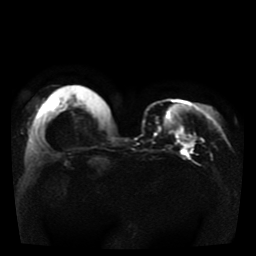
Breast MRI, one axial slice. Slice 12 of 41 in the series (ordered by position). Diffusion-weighted series; image 2 of 4 stored at this slice position (different b-values; order by instance number). 1.5 T. 5 mm slice thickness. 256 × 256 image matrix, field of view 330 × 330 mm. Female patient.
Annotated regions visible in this slice (outlined manually by an expert reader):
- tumour on diffusion-weighted imaging: bounding box [x1, y1, x2, y2] px = [177, 130, 193, 148]